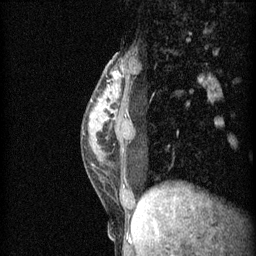
Breast MRI (dynamic contrast-enhanced), one sagittal slice; 3 images stored at this slice position (order not interpretable as contrast timing); 1.5 T; TE 4.2 ms, TR 11 ms; 256 × 256 image matrix, field of view 180 × 180 mm. Patient: female, 40 years.
Outlined on this slice (semi-automatically segmented with operator editing):
- analysis volume of interest (the breast-tissue region the enhancement analysis was run in; not a lesion): bounding box <82,54,140,191> (left, top, right, bottom; pixels)
- tumour enhancement mask (voxels above the 70 % enhancement threshold inside the analysis volume of interest): <115,72,117,77>